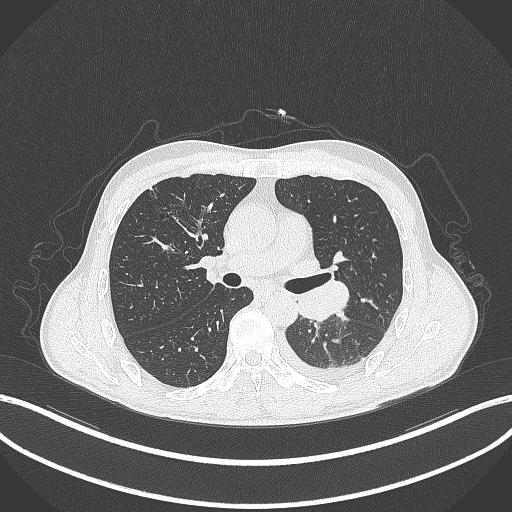
Chest CT, one axial slice. Slice 188 of 295 in the series (ordered by position). 120 kVp. Lung window (W 1500 / L -600 HU). 512 × 512 image matrix, field of view 400 × 400 mm. Patient: male, 47 years. From the clinical record (not read from this slice): clinical TNM (as recorded): T3 N1 M1c.
Outlined on this slice (bounding box drawn by a radiologist):
- lung tumour (recorded histology: small cell carcinoma): bounding box <295,281,352,323> (left, top, right, bottom; pixels)